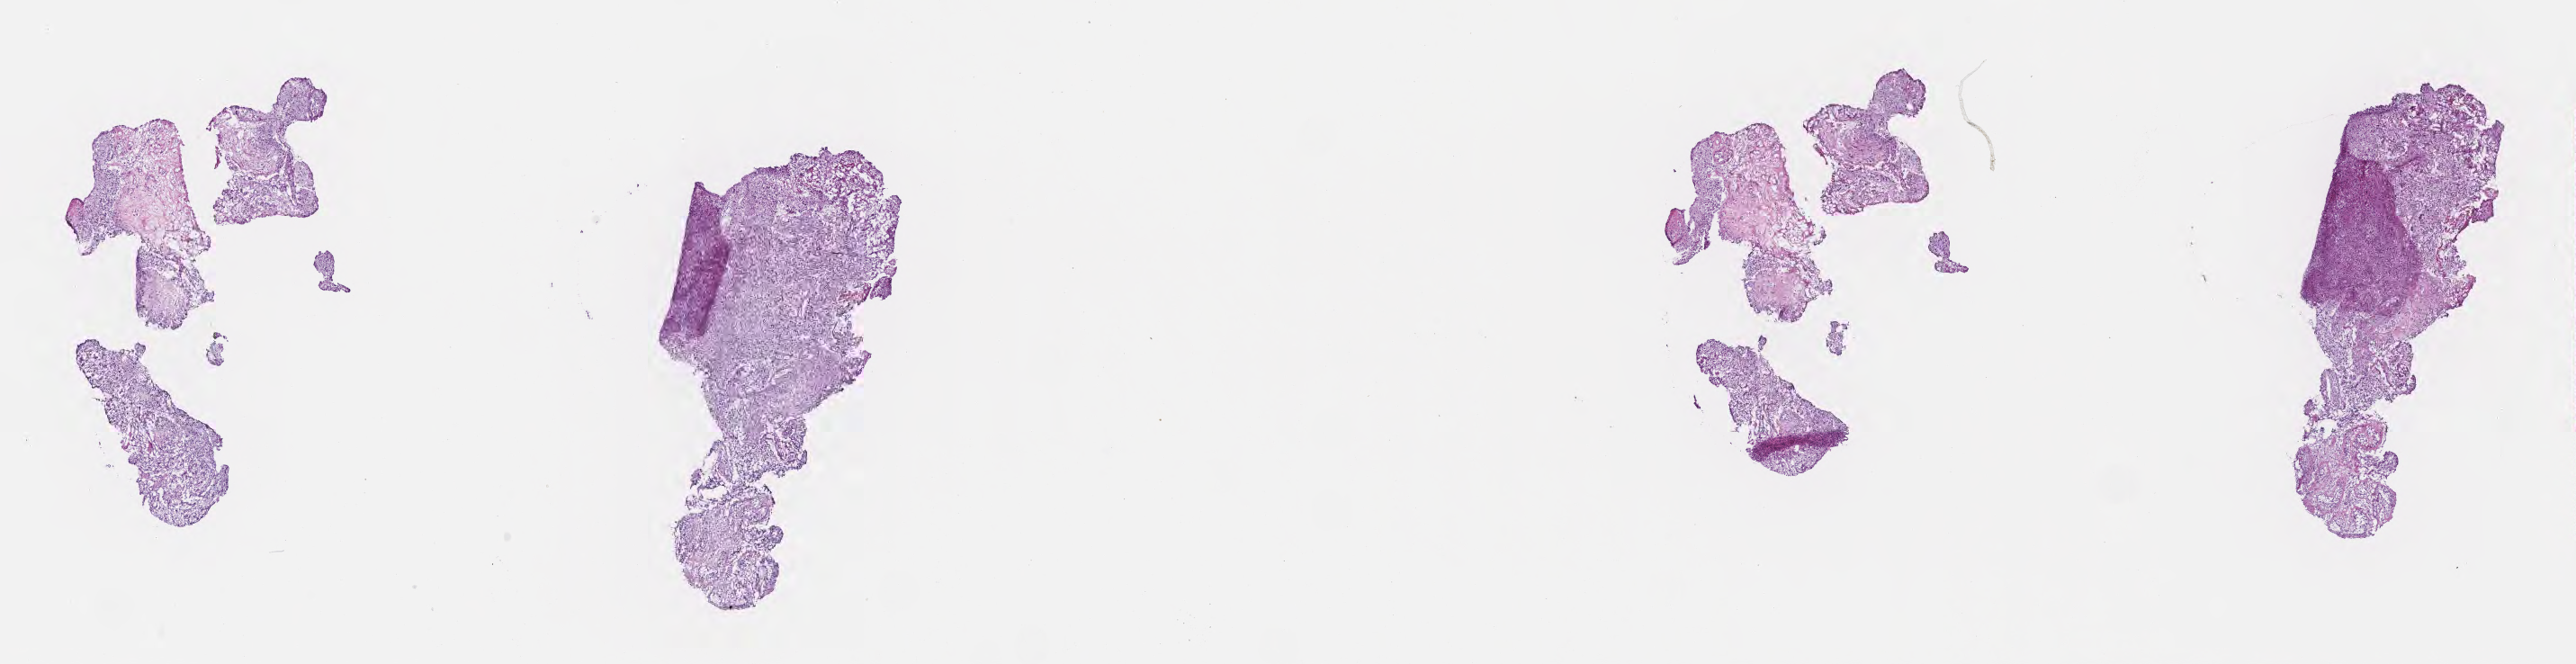
Whole-slide image, haematoxylin and eosin stain, whole scanned area (about 23.1 x 6.0 mm) shown as a low-resolution overview. Cryosection. Specimen: recurrent tumor. Anatomic site: brain. Patient: male, age at initial diagnosis 41 years. Pathologist review of this section (percent, as recorded): tumor cells 66%, tumor nuclei 68%, stromal cells 3%, necrosis 0%, normal cells 31%. Inflammatory infiltration, as recorded: lymphocyte infiltration 0%, monocyte infiltration 0%, neutrophil infiltration 0%.
* patient diagnosis: Glioblastoma, NOS
* section: bottom of the tissue portion